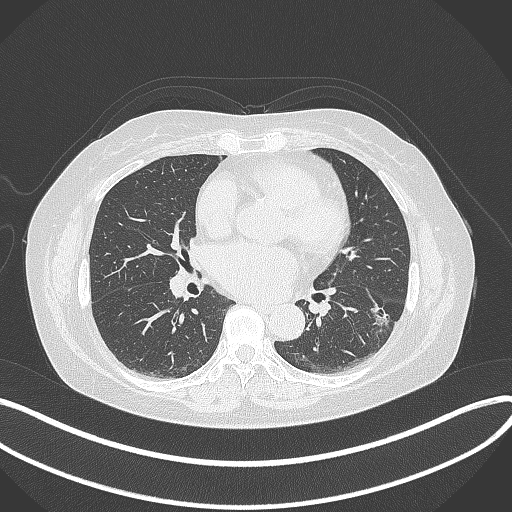
Chest CT, one axial slice; slice 172 of 373 in the series (ordered by position); reconstruction kernel B70f; 120 kVp; lung window (W 1500 / L -600 HU); 512 × 512 image matrix, field of view 400 × 400 mm. Patient: female, 67 years. From the clinical record (not read from this slice): clinical TNM (as recorded): T1c N0 M0.
Outlined on this slice (rectangle marked by the reading radiologist):
- lung tumour (recorded histology: adenocarcinoma): bounding box <365,299,394,332> (left, top, right, bottom; pixels)